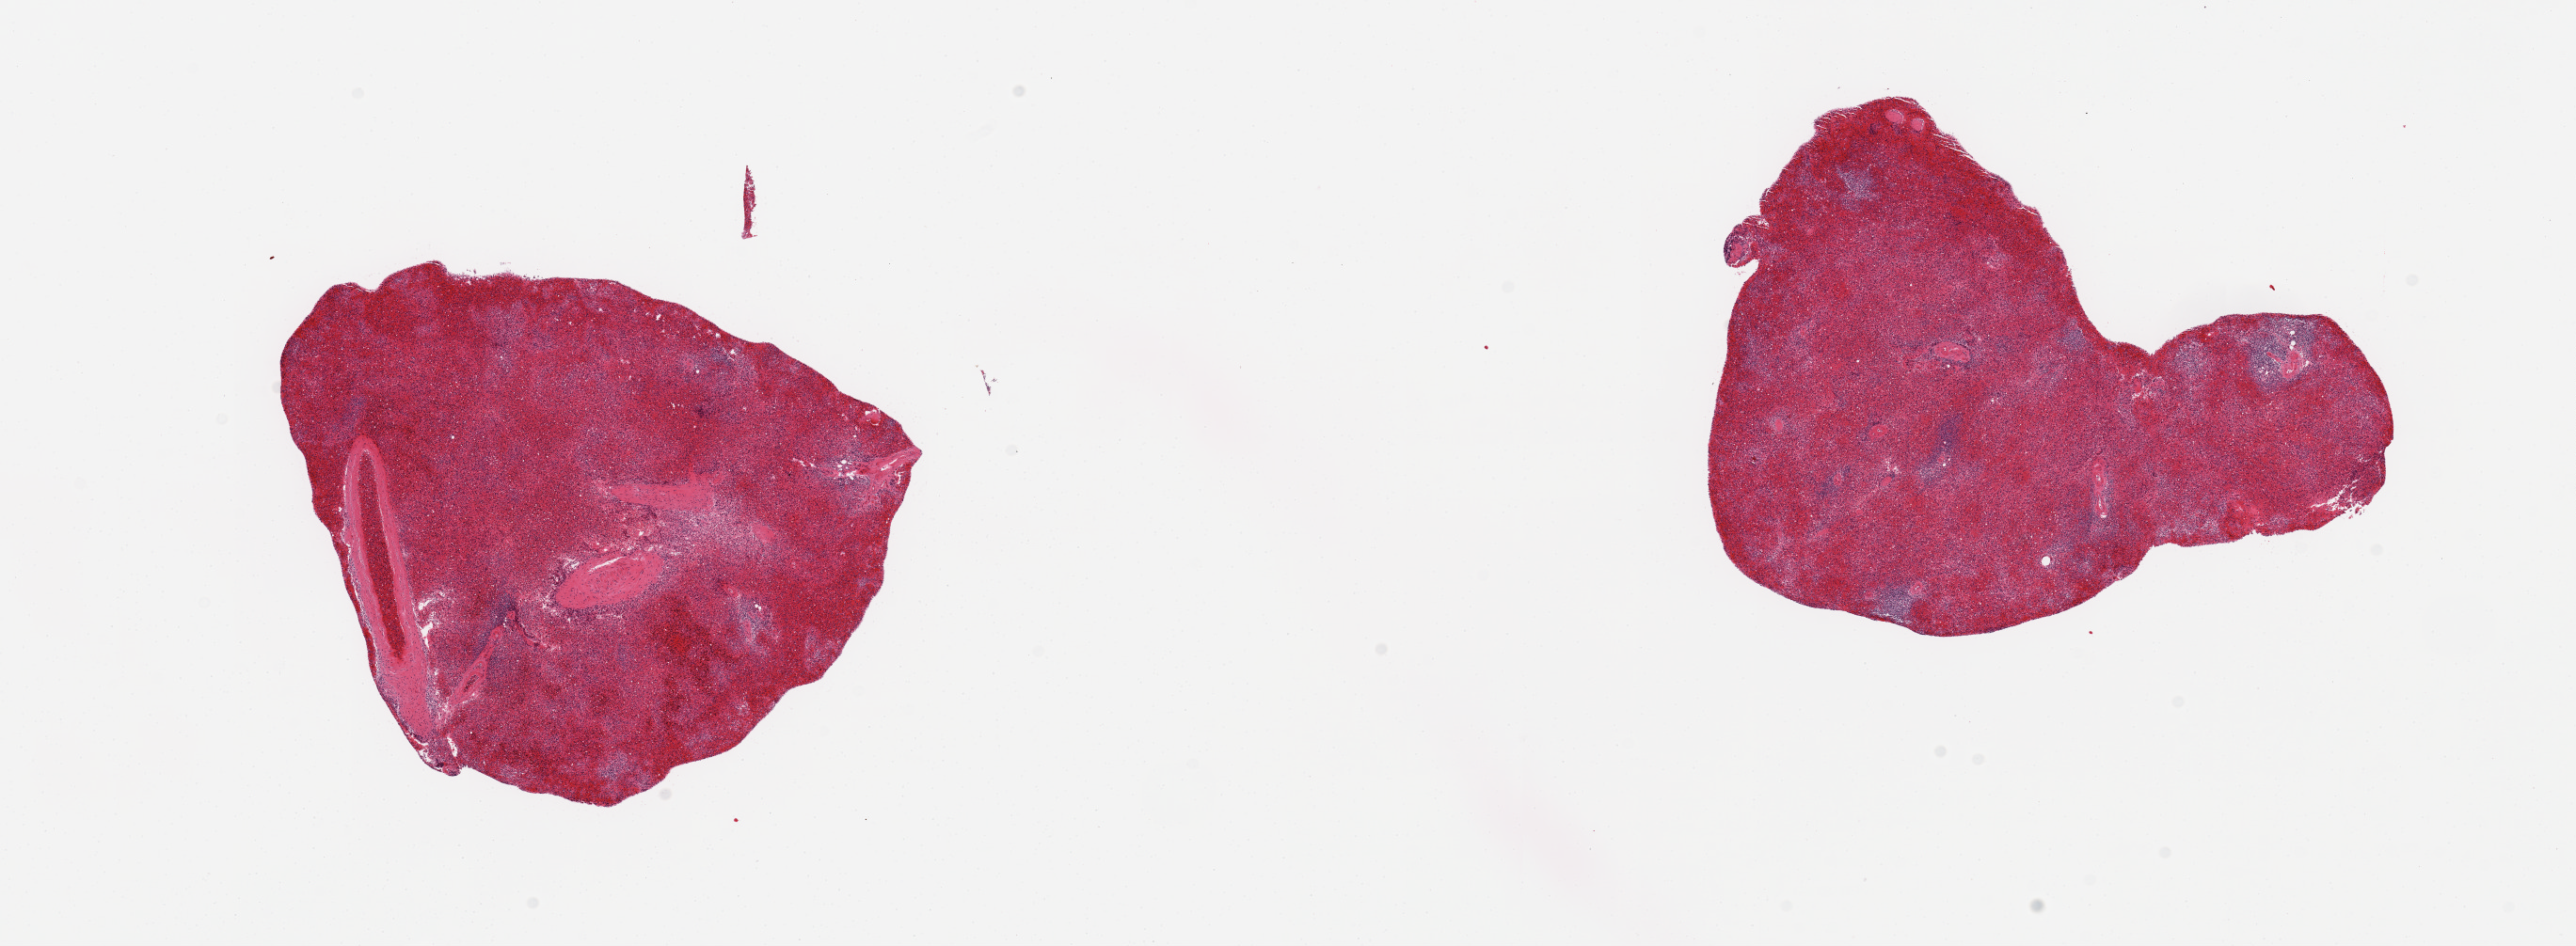
Whole-slide image, hematoxylin and eosin (H&E) stain, a low-resolution overview of the entire scanned area, about 21.7 x 8.0 mm; PAXgene-fixed, paraffin-embedded tissue; section of spleen (target tissue); donor tissue sample. Donor sex: male.
Reviewer comment on this tissue sample: 2 pieces; marked congestion.